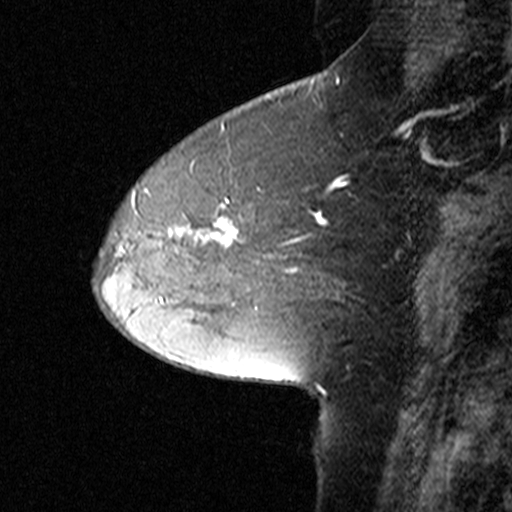
Breast MRI (dynamic contrast-enhanced), one sagittal slice. Slice 16 of 44 in the series (ordered by position). Dynamic contrast-enhanced study with each time point stored as its own series, time point 2 of 3 at this slice position (early post-contrast, ordered by acquisition time). 1.5 T. TE 4.5 ms, TR 11 ms. 3 mm slice thickness. 512 × 512 image matrix. Female patient, age 50 years. From the clinical record (not read from this slice): setting: breast cancer imaged before/during neoadjuvant chemotherapy; receptor status: HR-positive, HER2-negative.
Annotated regions visible in this slice (semi-automatically segmented with operator editing):
- analysis volume of interest (the breast-tissue region the enhancement analysis was run in; not a lesion): box from (x=126, y=162) to (x=306, y=291) px
- tumour enhancement mask (voxels above the 90 % enhancement threshold inside the analysis volume of interest): (x=132, y=189)–(x=295, y=272)